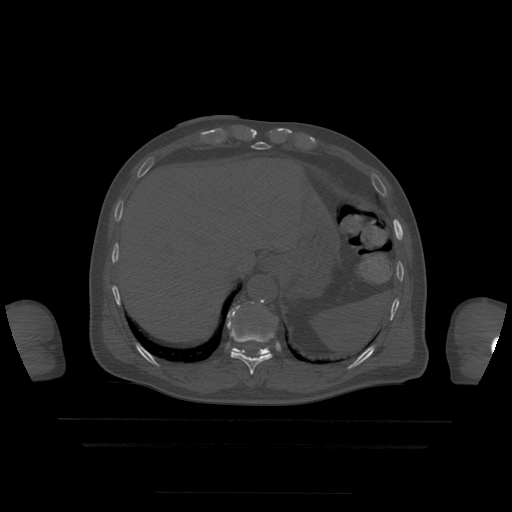
CT including the spine, one axial slice. Position 234 of 522 along the scan axis. Bone window (W 1800 / L 400 HU). 1.25 mm slice thickness. 512 × 512 image matrix, field of view 436 × 436 mm. Patient age 68 years. From the clinical record (not read from this slice): primary cancer: urothelial.
Structures marked on this image (semi-automatic segmentation, software-assisted and operator-edited):
- T10 vertebra: bounding box [x1, y1, x2, y2] px = [227, 306, 274, 375]
- T11 vertebra: [232, 302, 271, 357]